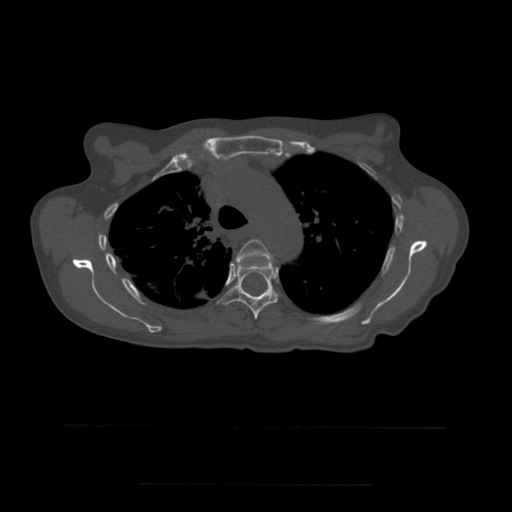
CT including the spine, one axial slice. Position 395 of 544 along the scan axis. Bone window (W 1800 / L 400 HU). 512 × 512 image matrix, field of view 350 × 350 mm. Patient age 58 years. From the clinical record (not read from this slice): primary cancer: lung.
Structures marked on this image (semi-automatically segmented with operator editing):
- T4 vertebra: box from (x=236, y=240) to (x=274, y=265) px
- T5 vertebra: (x=218, y=259)–(x=279, y=320)